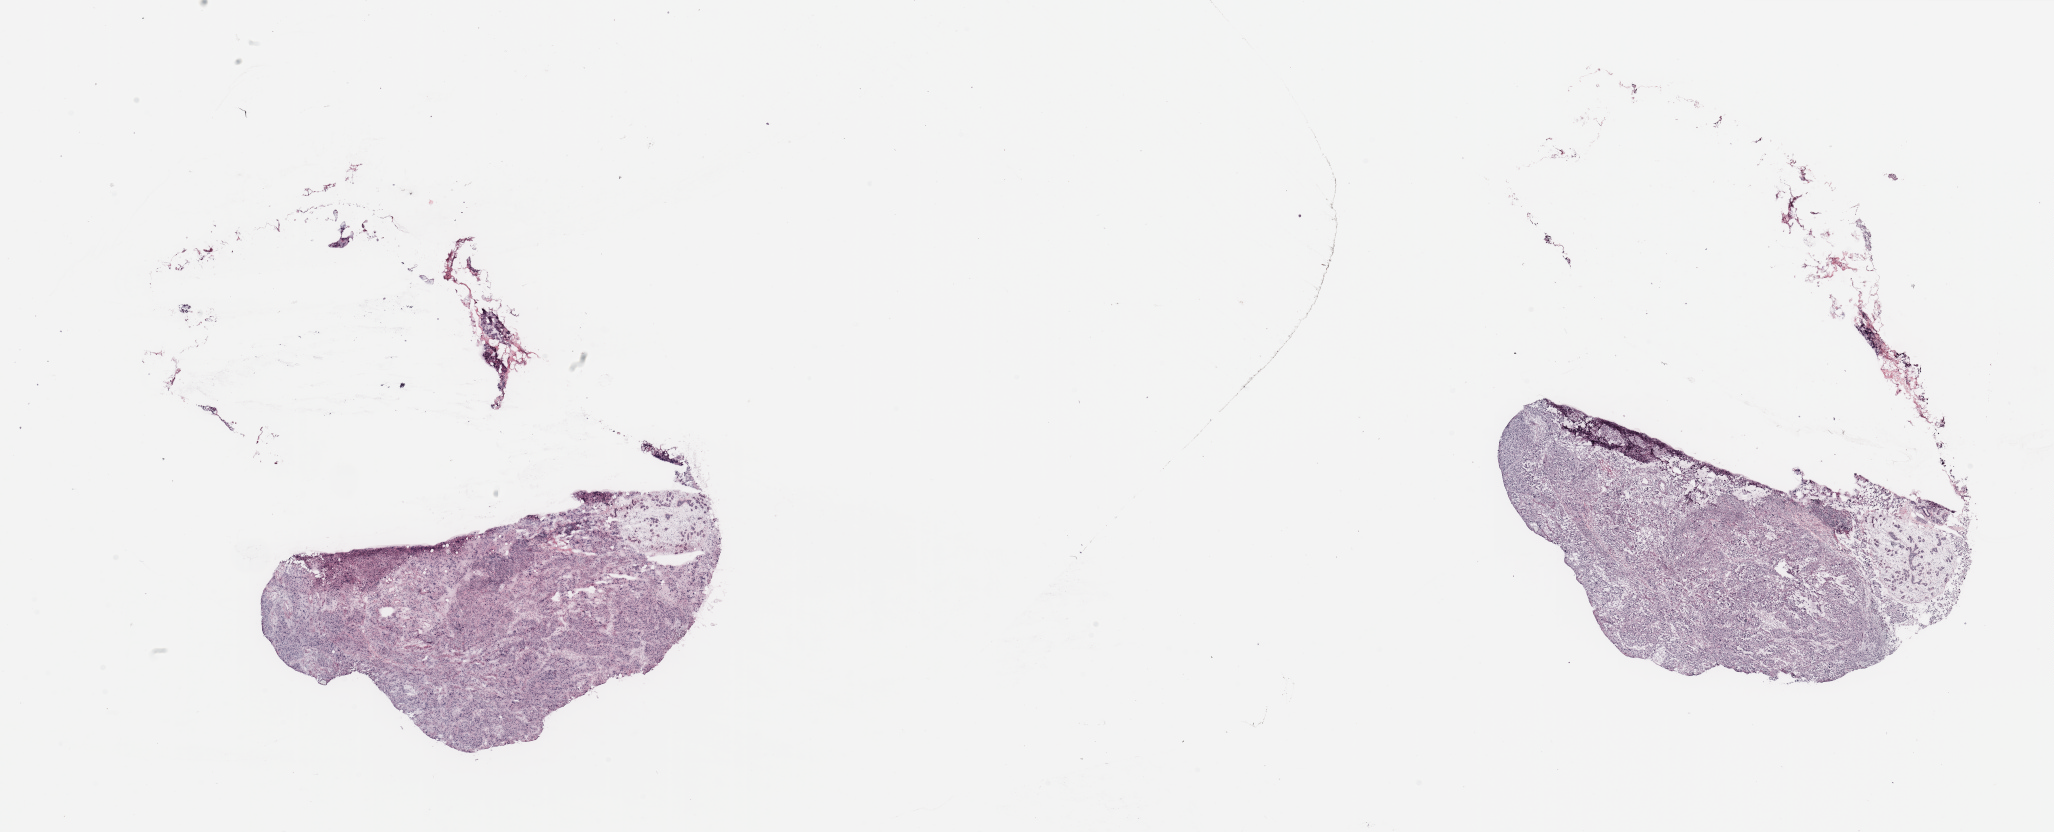
H&E-stained whole-slide image — low-resolution overview of the scanned area, about 32.5 x 13.2 mm (slide scanned at 20x), breast, tissue type not recorded.
- patient diagnosis (cohort enrolment): breast cancer (breast)